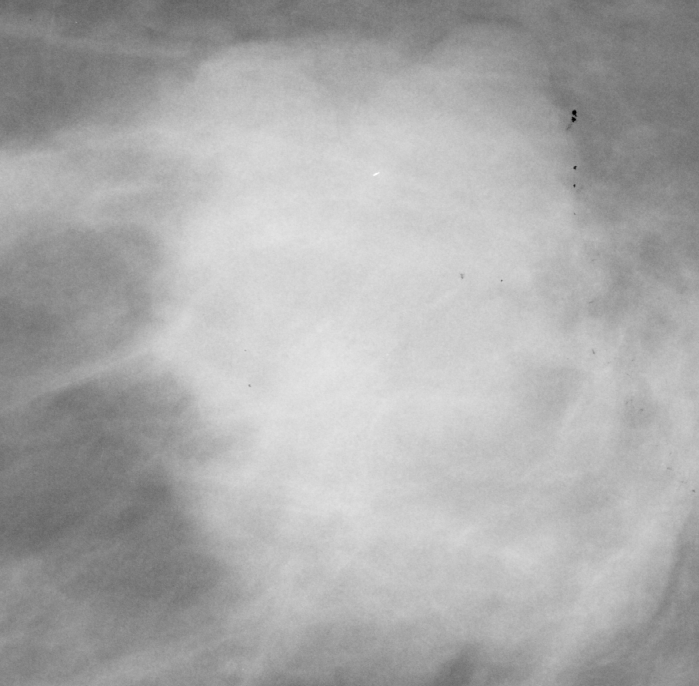
Region of interest cut from a scanned film mammogram (one marked finding), right breast, MLO view.
Finding: mass, shape lobulated, margins microlobulated; BI-RADS assessment category 5; pathology (as recorded): malignant.